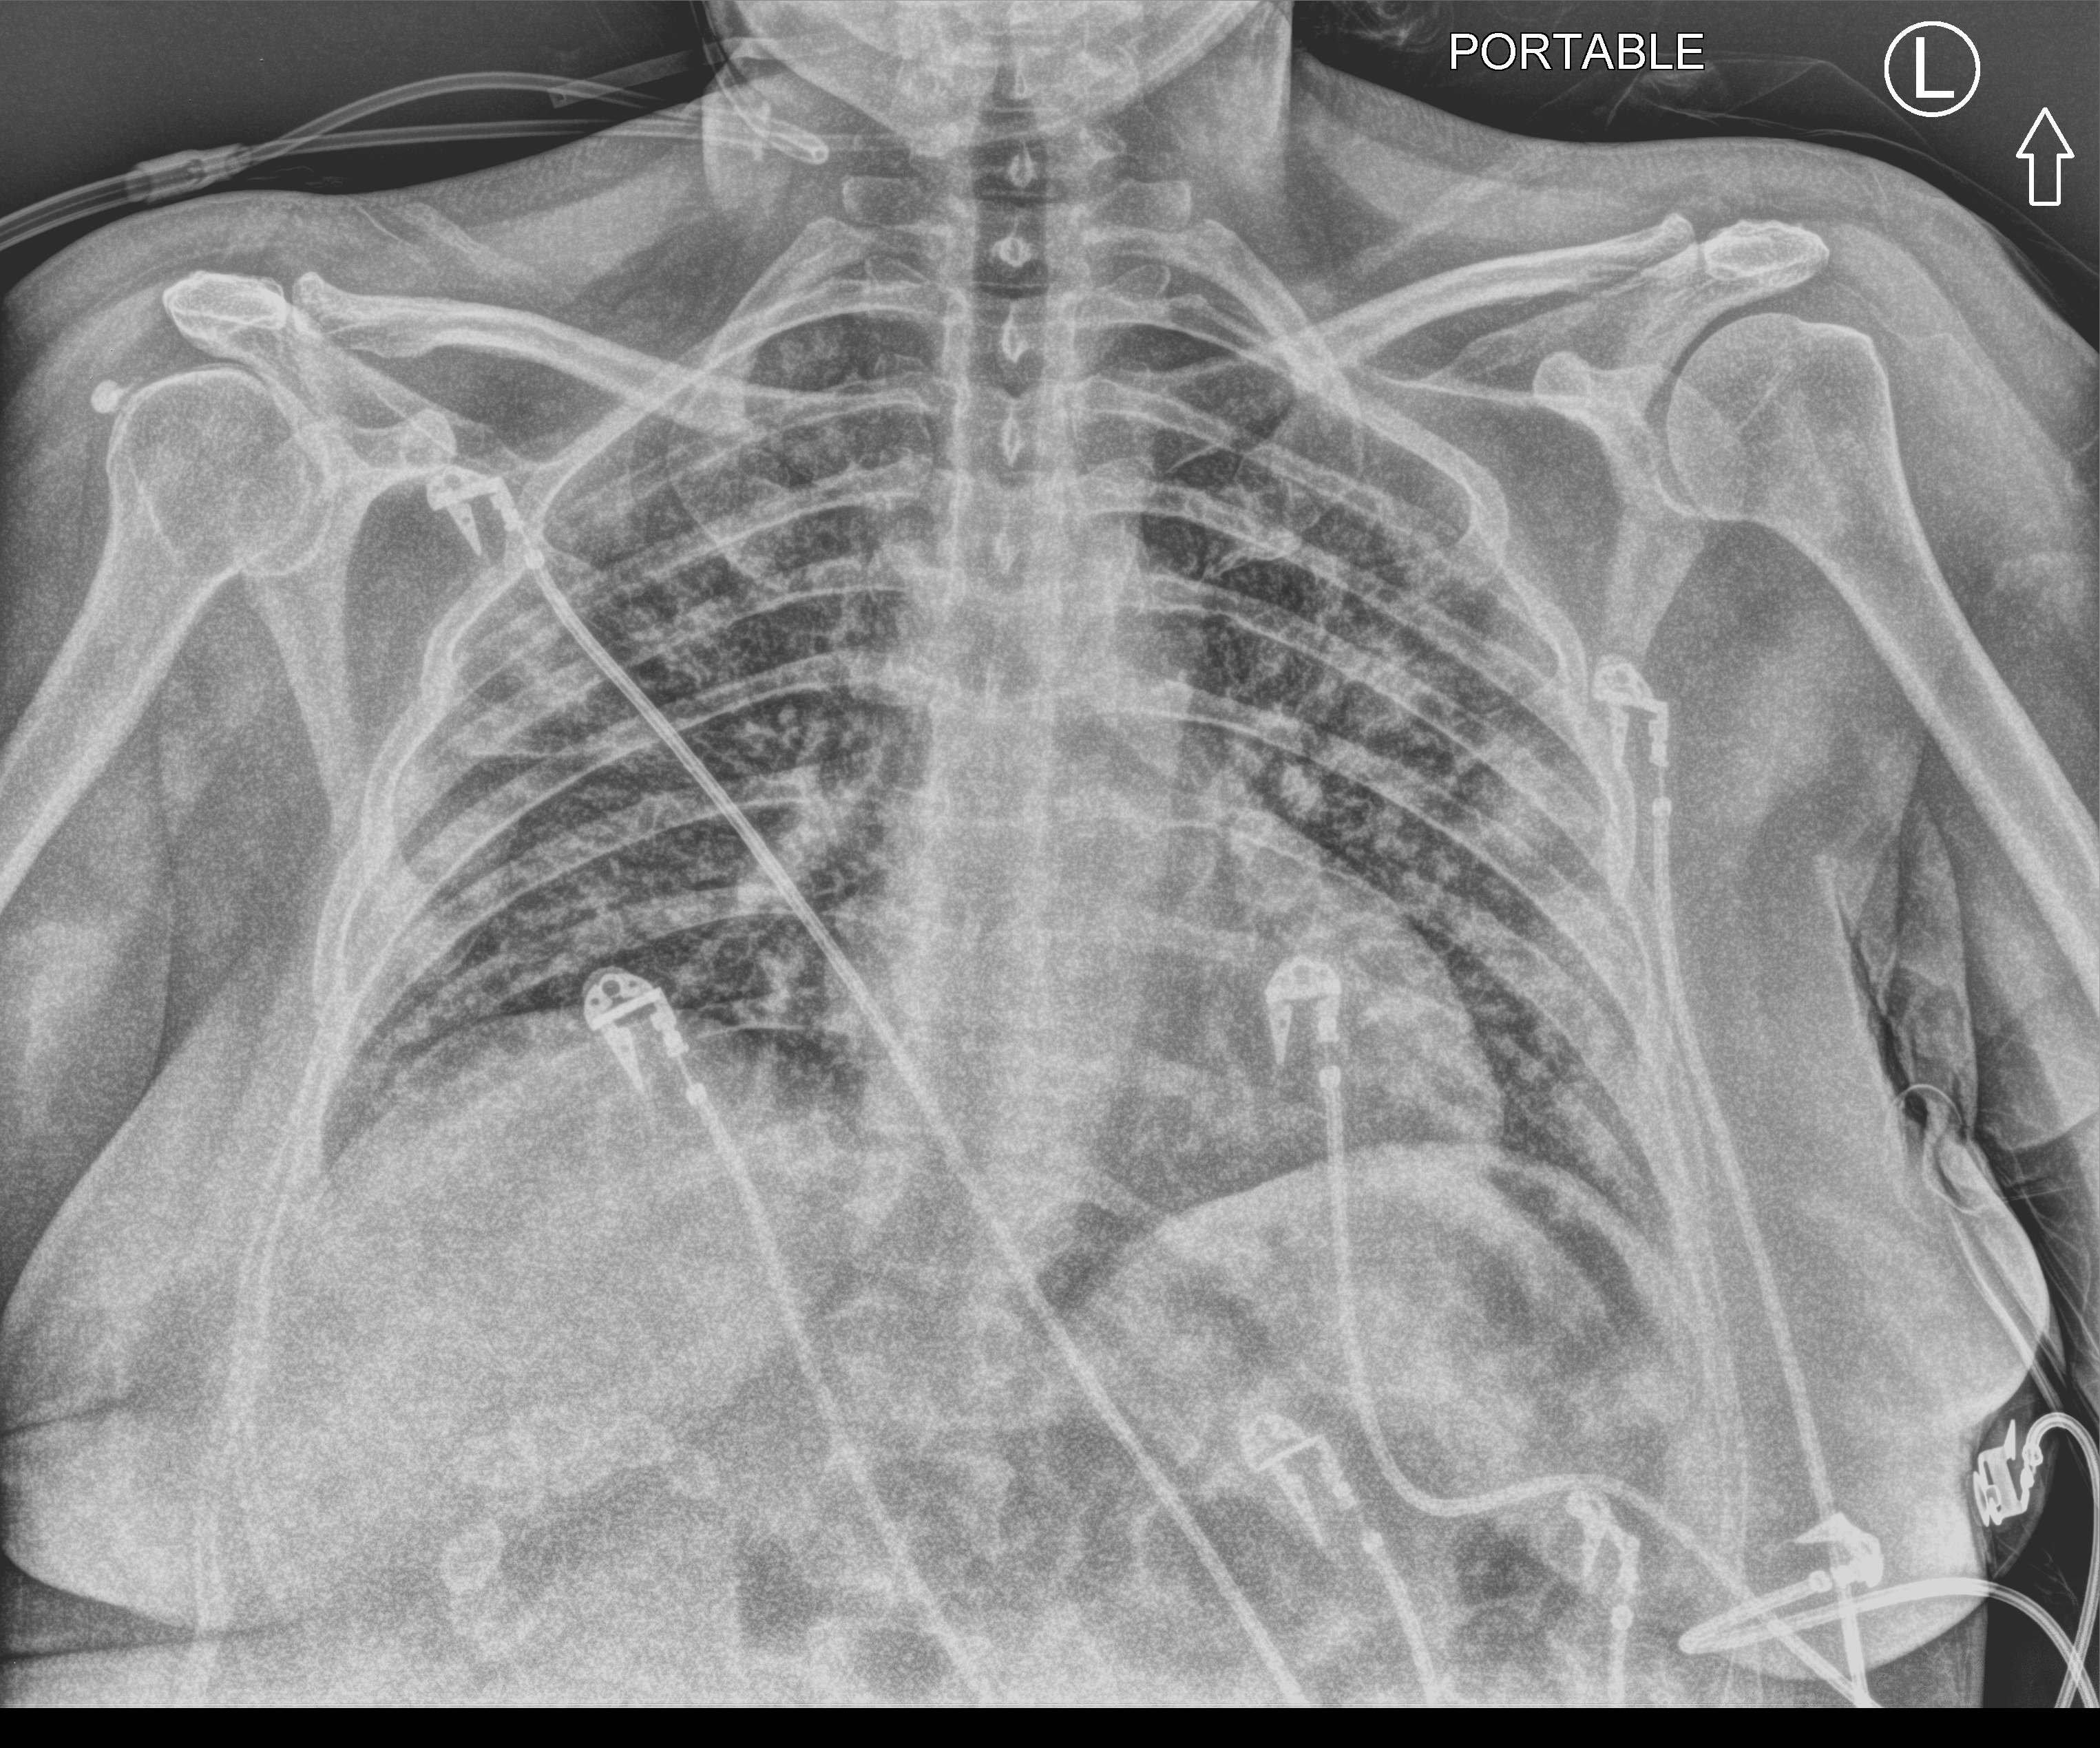
Chest X-ray (portable), anteroposterior (AP) projection. Patient hospitalised with COVID-19; female, aged 18–59 years.
Admission-level facts for this patient (not findings on this image; timing relative to this image not recorded): mechanically ventilated during this hospital stay: no.